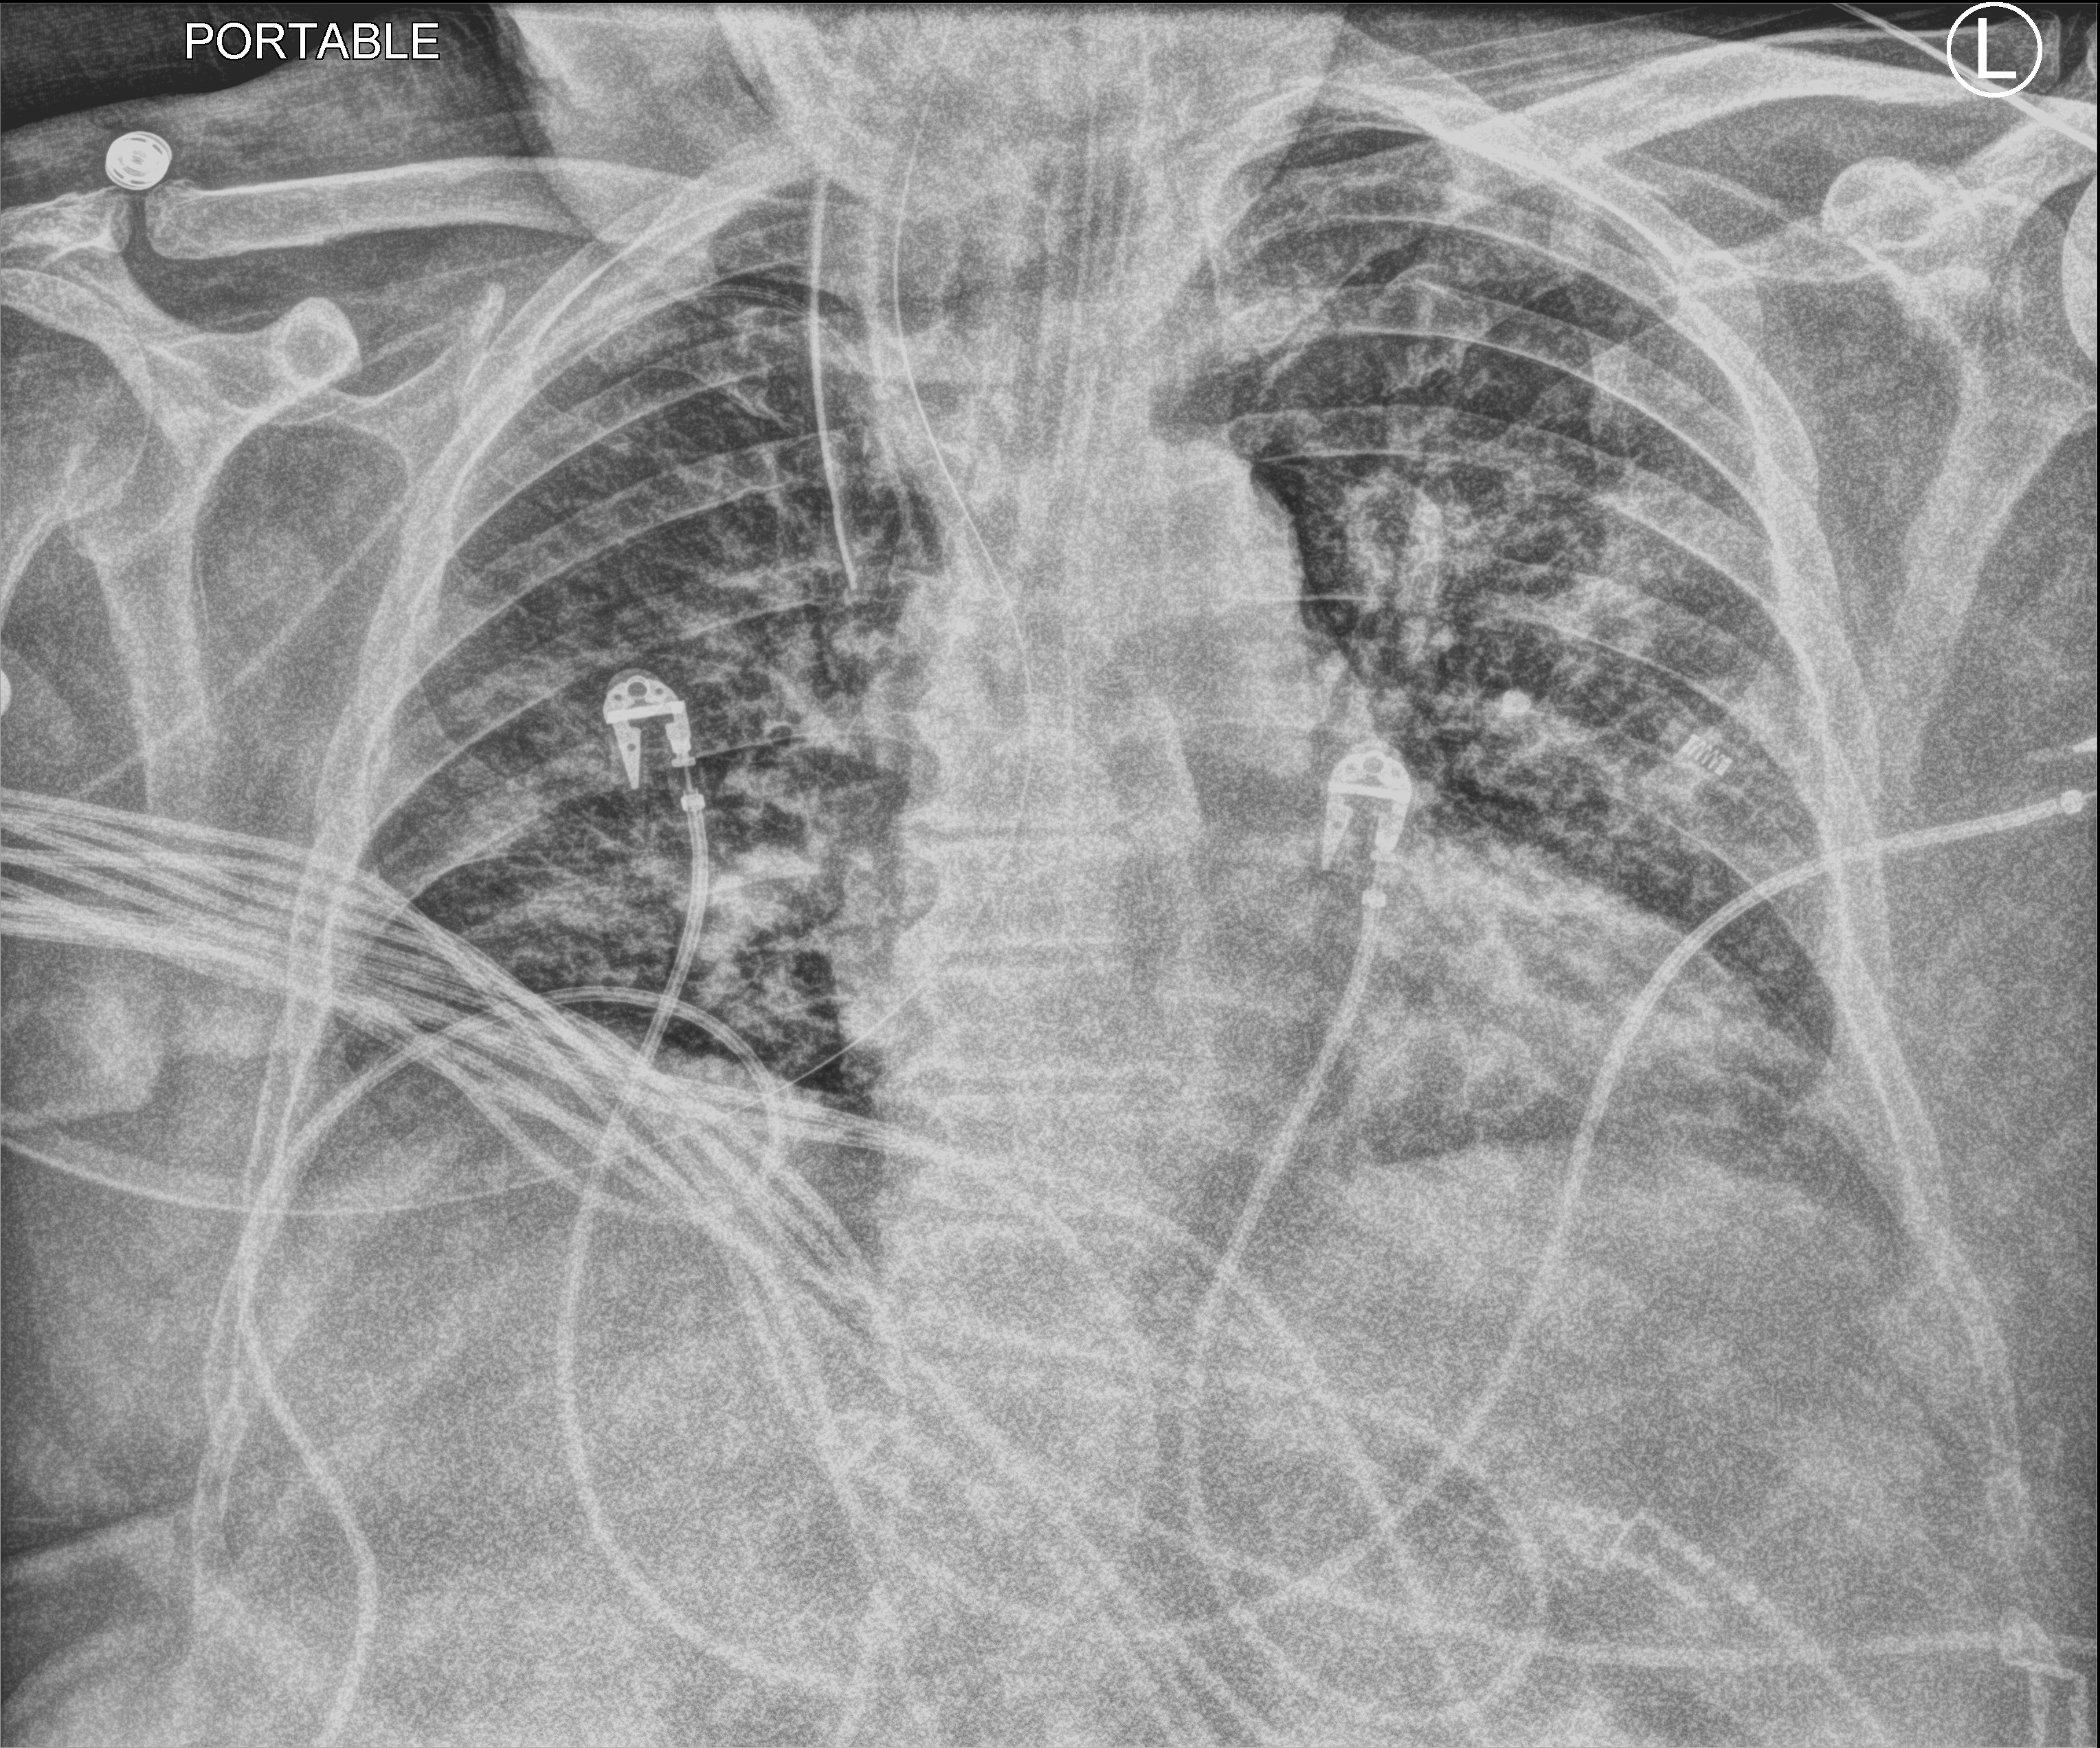
Bedside chest radiograph (computed radiography); anteroposterior (AP) projection. Patient hospitalised with COVID-19; male, aged 60–74 years.
From the hospital-stay record, not from the radiograph (when in the stay this image was taken is not recorded): admitted to intensive care during this hospital stay: yes; mechanically ventilated during this hospital stay: yes.